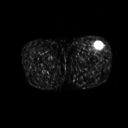
FDG PET of an extremity soft-tissue mass (from a PET/CT study), one axial slice. Slice 222 of 267 in the series (ordered by position). 3.27 mm slice thickness. 128 × 128 image matrix, field of view 500 × 500 mm. Patient: male, 64 years. Case-level facts recorded for this patient, not image findings: histological type: extraskeletal osteosarcoma; grade: high; site of the primary tumour: thigh.
Structures marked on this image (expert contour drawn on MRI and transferred to this co-registered scan by the dataset authors):
- gross tumour volume (mass): box from (x=93, y=43) to (x=103, y=51) px